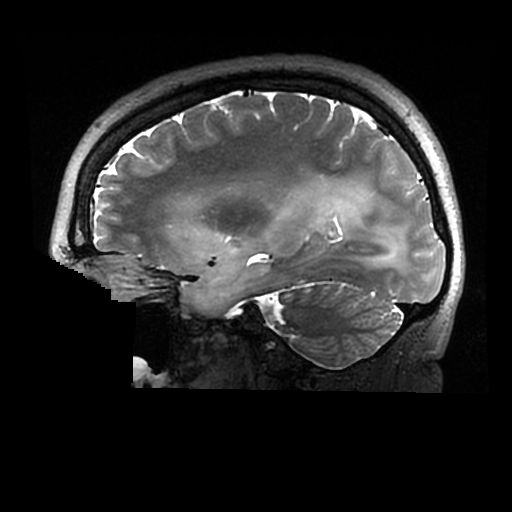
Brain MRI from a brain-tumour surgery series, one sagittal slice. Position 191 of 320 along the scan axis. 0.6 mm slice thickness. 512 × 512 image matrix, field of view 240 × 240 mm. From the clinical record (not read from this slice): histopathology: Astrocytoma; WHO grade: 2; IDH mutation: yes.
Structures marked on this image (expert manual segmentation):
- tumour: bounding box [x1, y1, x2, y2] px = [174, 183, 407, 314]